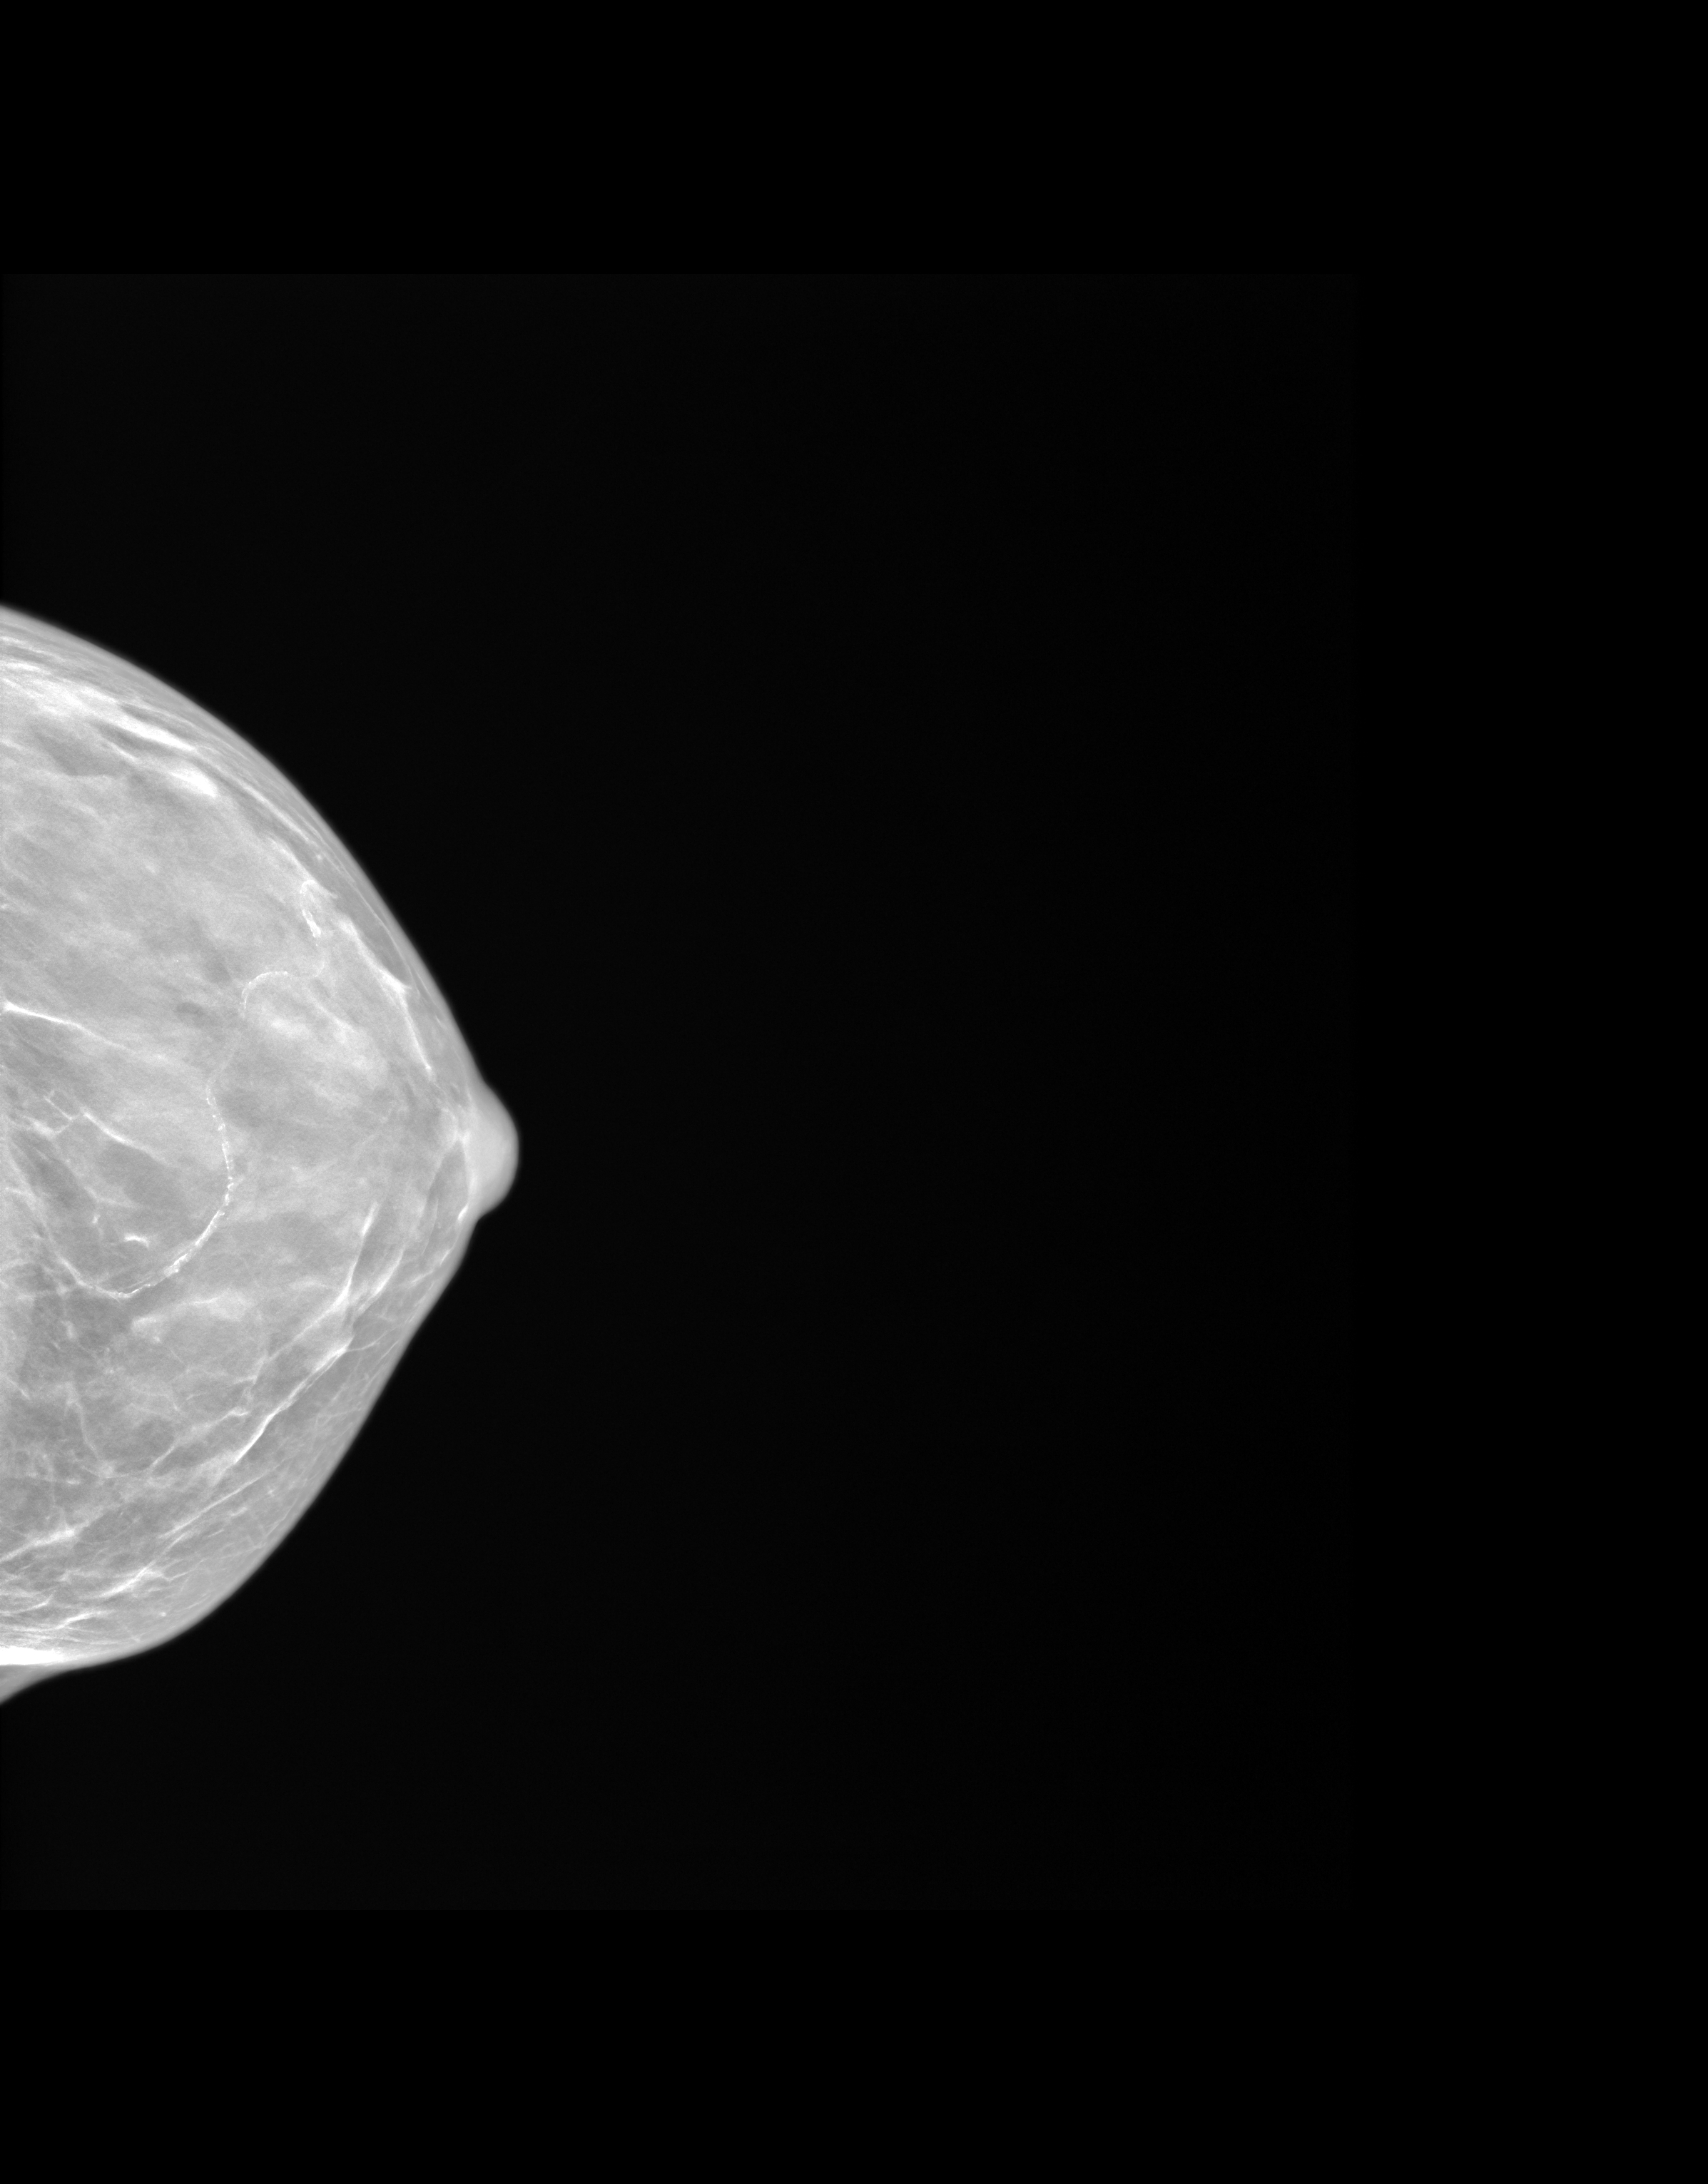
Synthesized 2-D mammogram reconstructed from digital breast tomosynthesis, left breast, cranio-caudal projection, annual screening mammography examination. Female patient, age 59 years.
BI-RADS breast density category at the screening exam (both breasts, scale 1–4): 4. Final BI-RADS category for the screening round (tomosynthesis exam, both breasts): category 1. Recall: no recall after this screen.